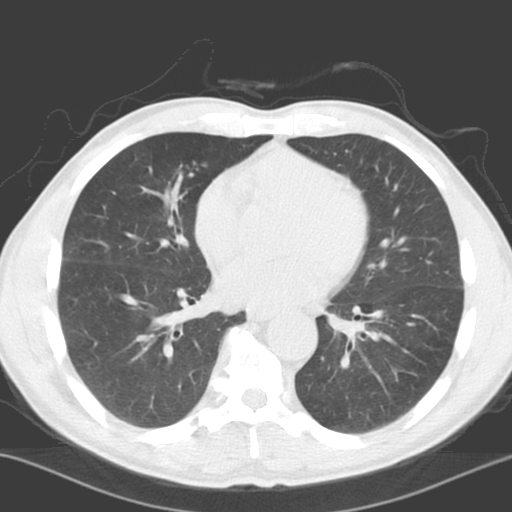
Low-dose screening chest CT, axial slice. Baseline screening round. Lung window (W 1500 / L -600 HU). 3.2 mm slice thickness. Standard (soft-tissue) reconstruction kernel (C). Slice 102 of 178 in the series. 512 × 512 image matrix. Male participant, aged 65 years at enrolment. Current smoker at enrolment.
Expert reader's lesion annotation, bounding box [x1, y1, x2, y2] px = [141, 159, 202, 223]. Screening reader's record for this exam (one nodule recorded; not confirmed to be the boxed lesion): non-calcified nodule or mass ≥4 mm, right lower lobe, 5 × 5 mm, poorly defined margins, soft tissue attenuation. Official screen result: positive, change unspecified: nodule(s) >= 4 mm or enlarging nodule(s), mass(es), or other non-specific abnormalities suspicious for lung cancer. Lung cancer was diagnosed 1144 days after this screen: squamous cell carcinoma, NOS, right middle lobe, poorly differentiated (G3), stage IA (AJCC 6th edition), 23 mm at pathology.